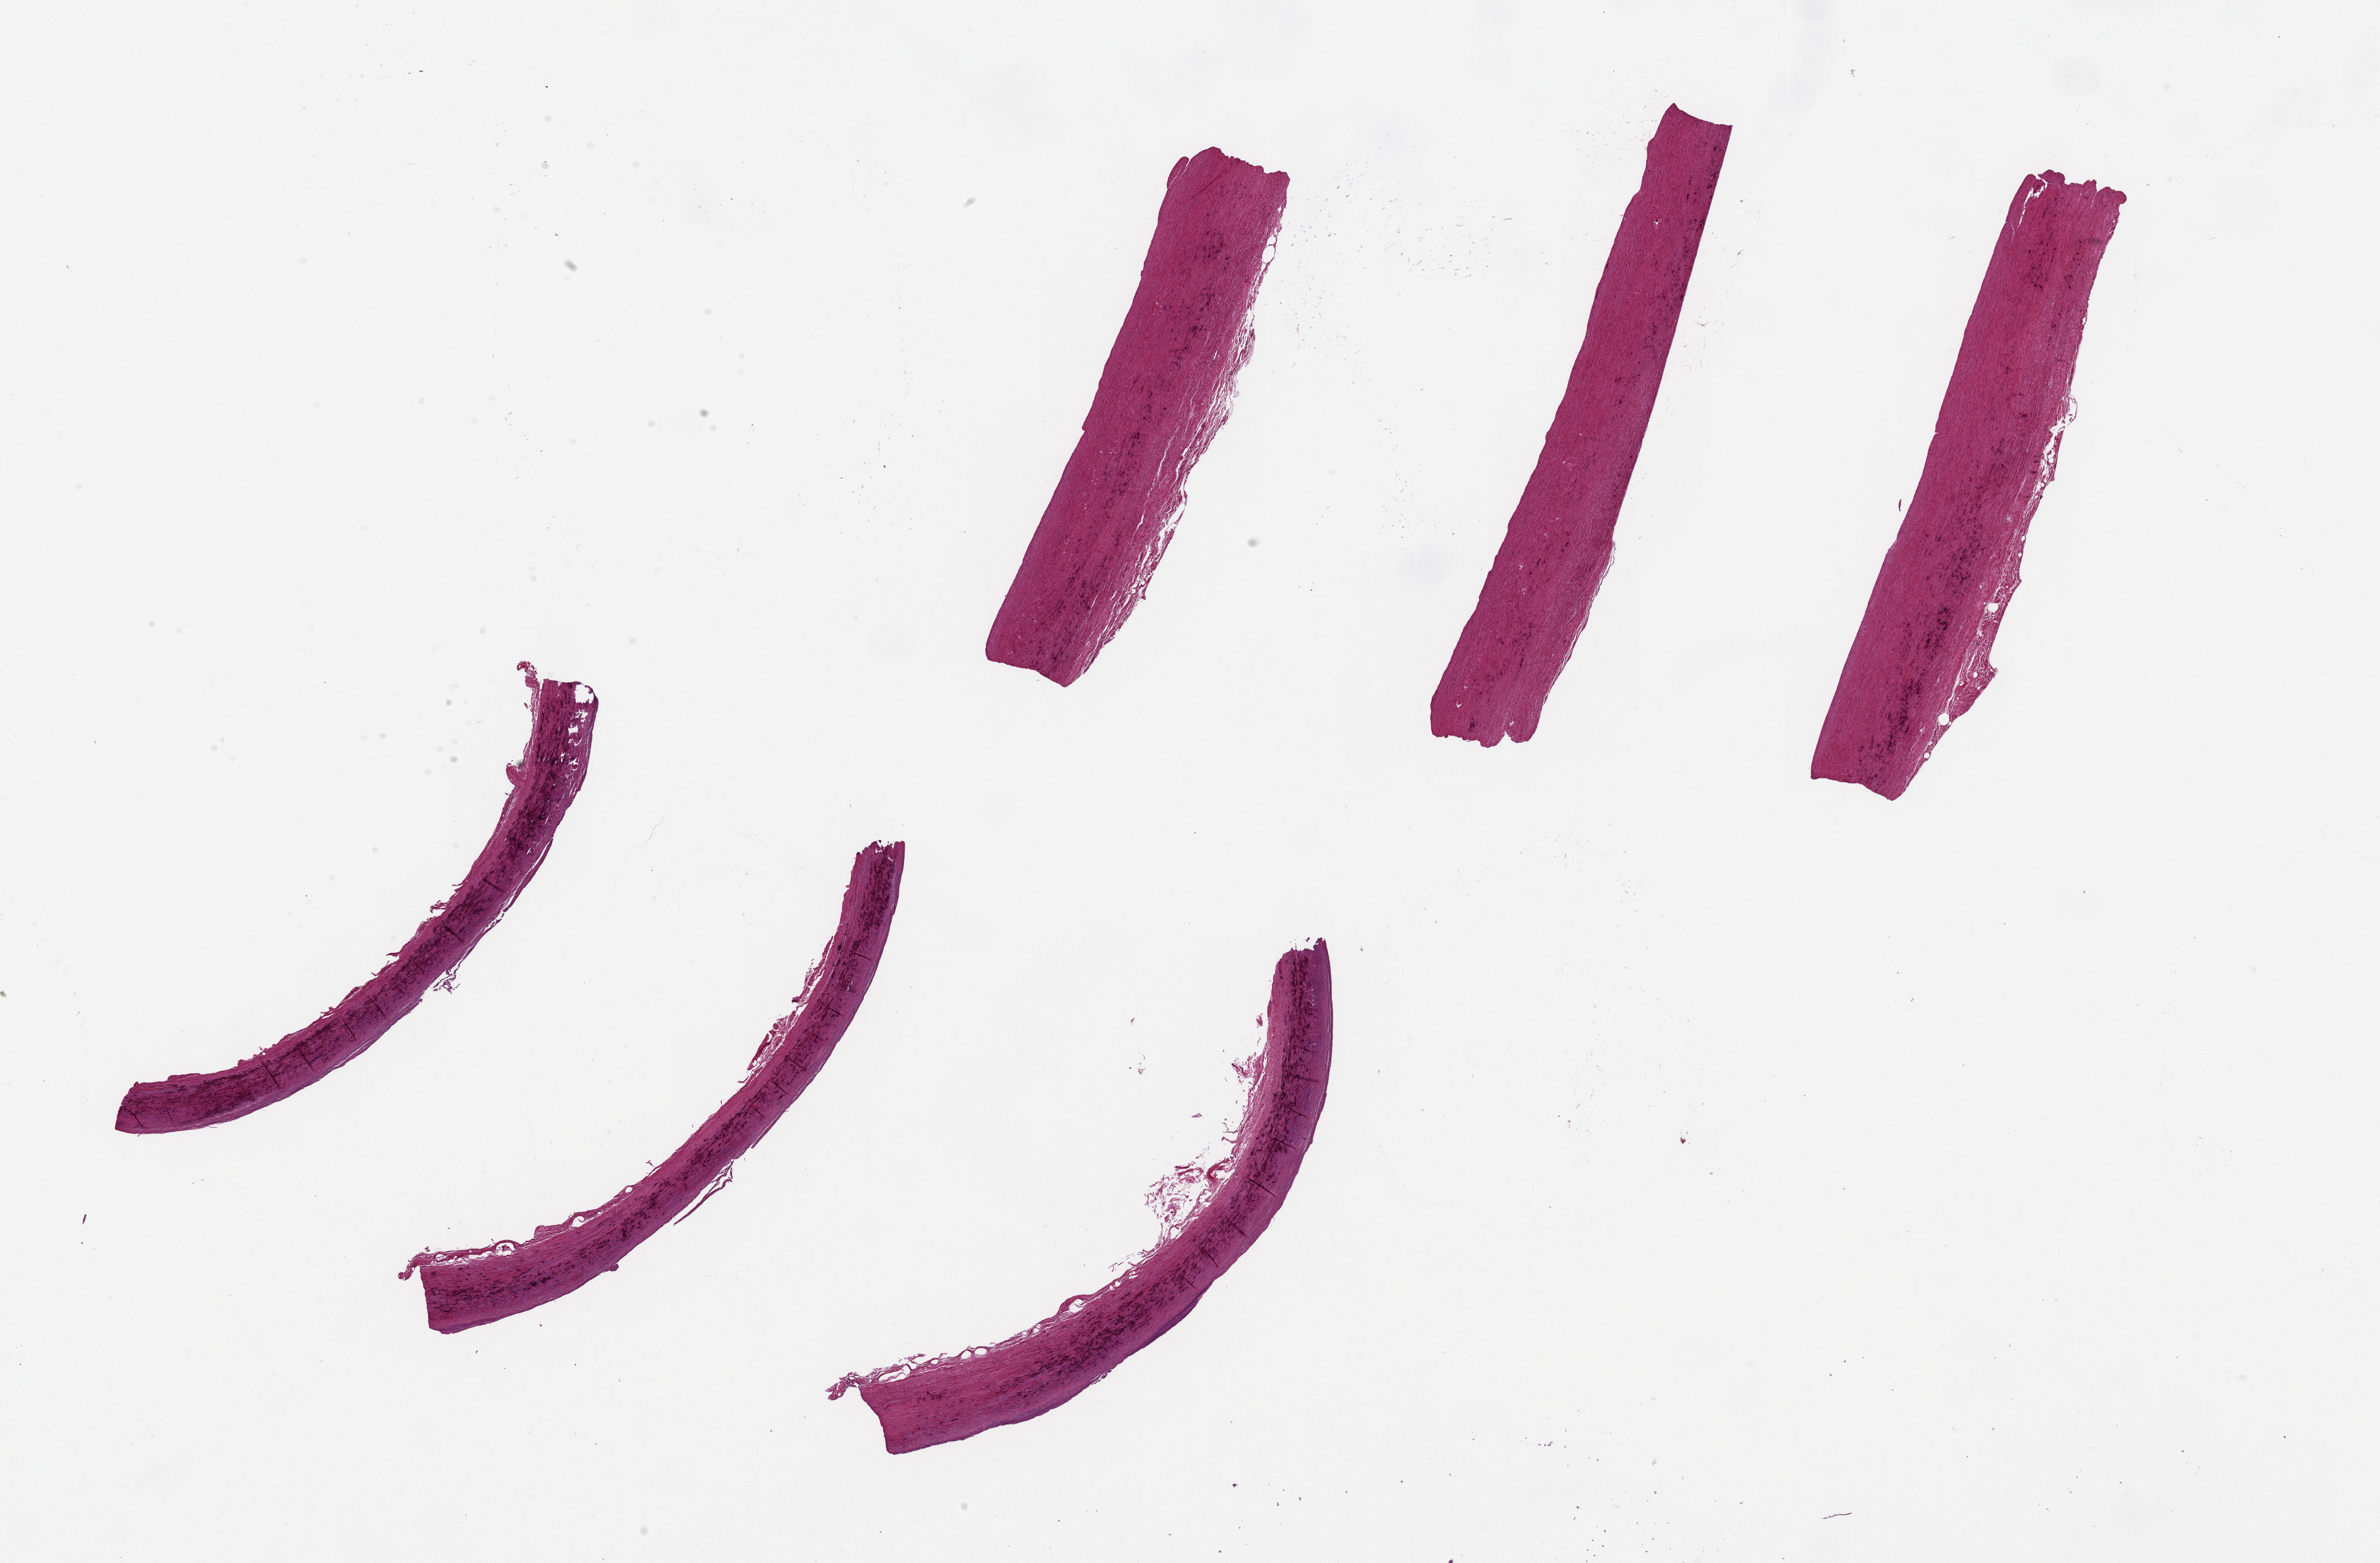
Digitized haematoxylin and eosin-stained section, low-resolution overview of the scanned area, about 31.5 x 20.7 mm (acquisition: 20x scan); PAXgene-fixed, paraffin-embedded tissue; sampled site (target tissue): aorta; donor tissue sample. Male donor.
- review note (as recorded): 6 pieces up to 9x1.7 mm; scattered medial calcification